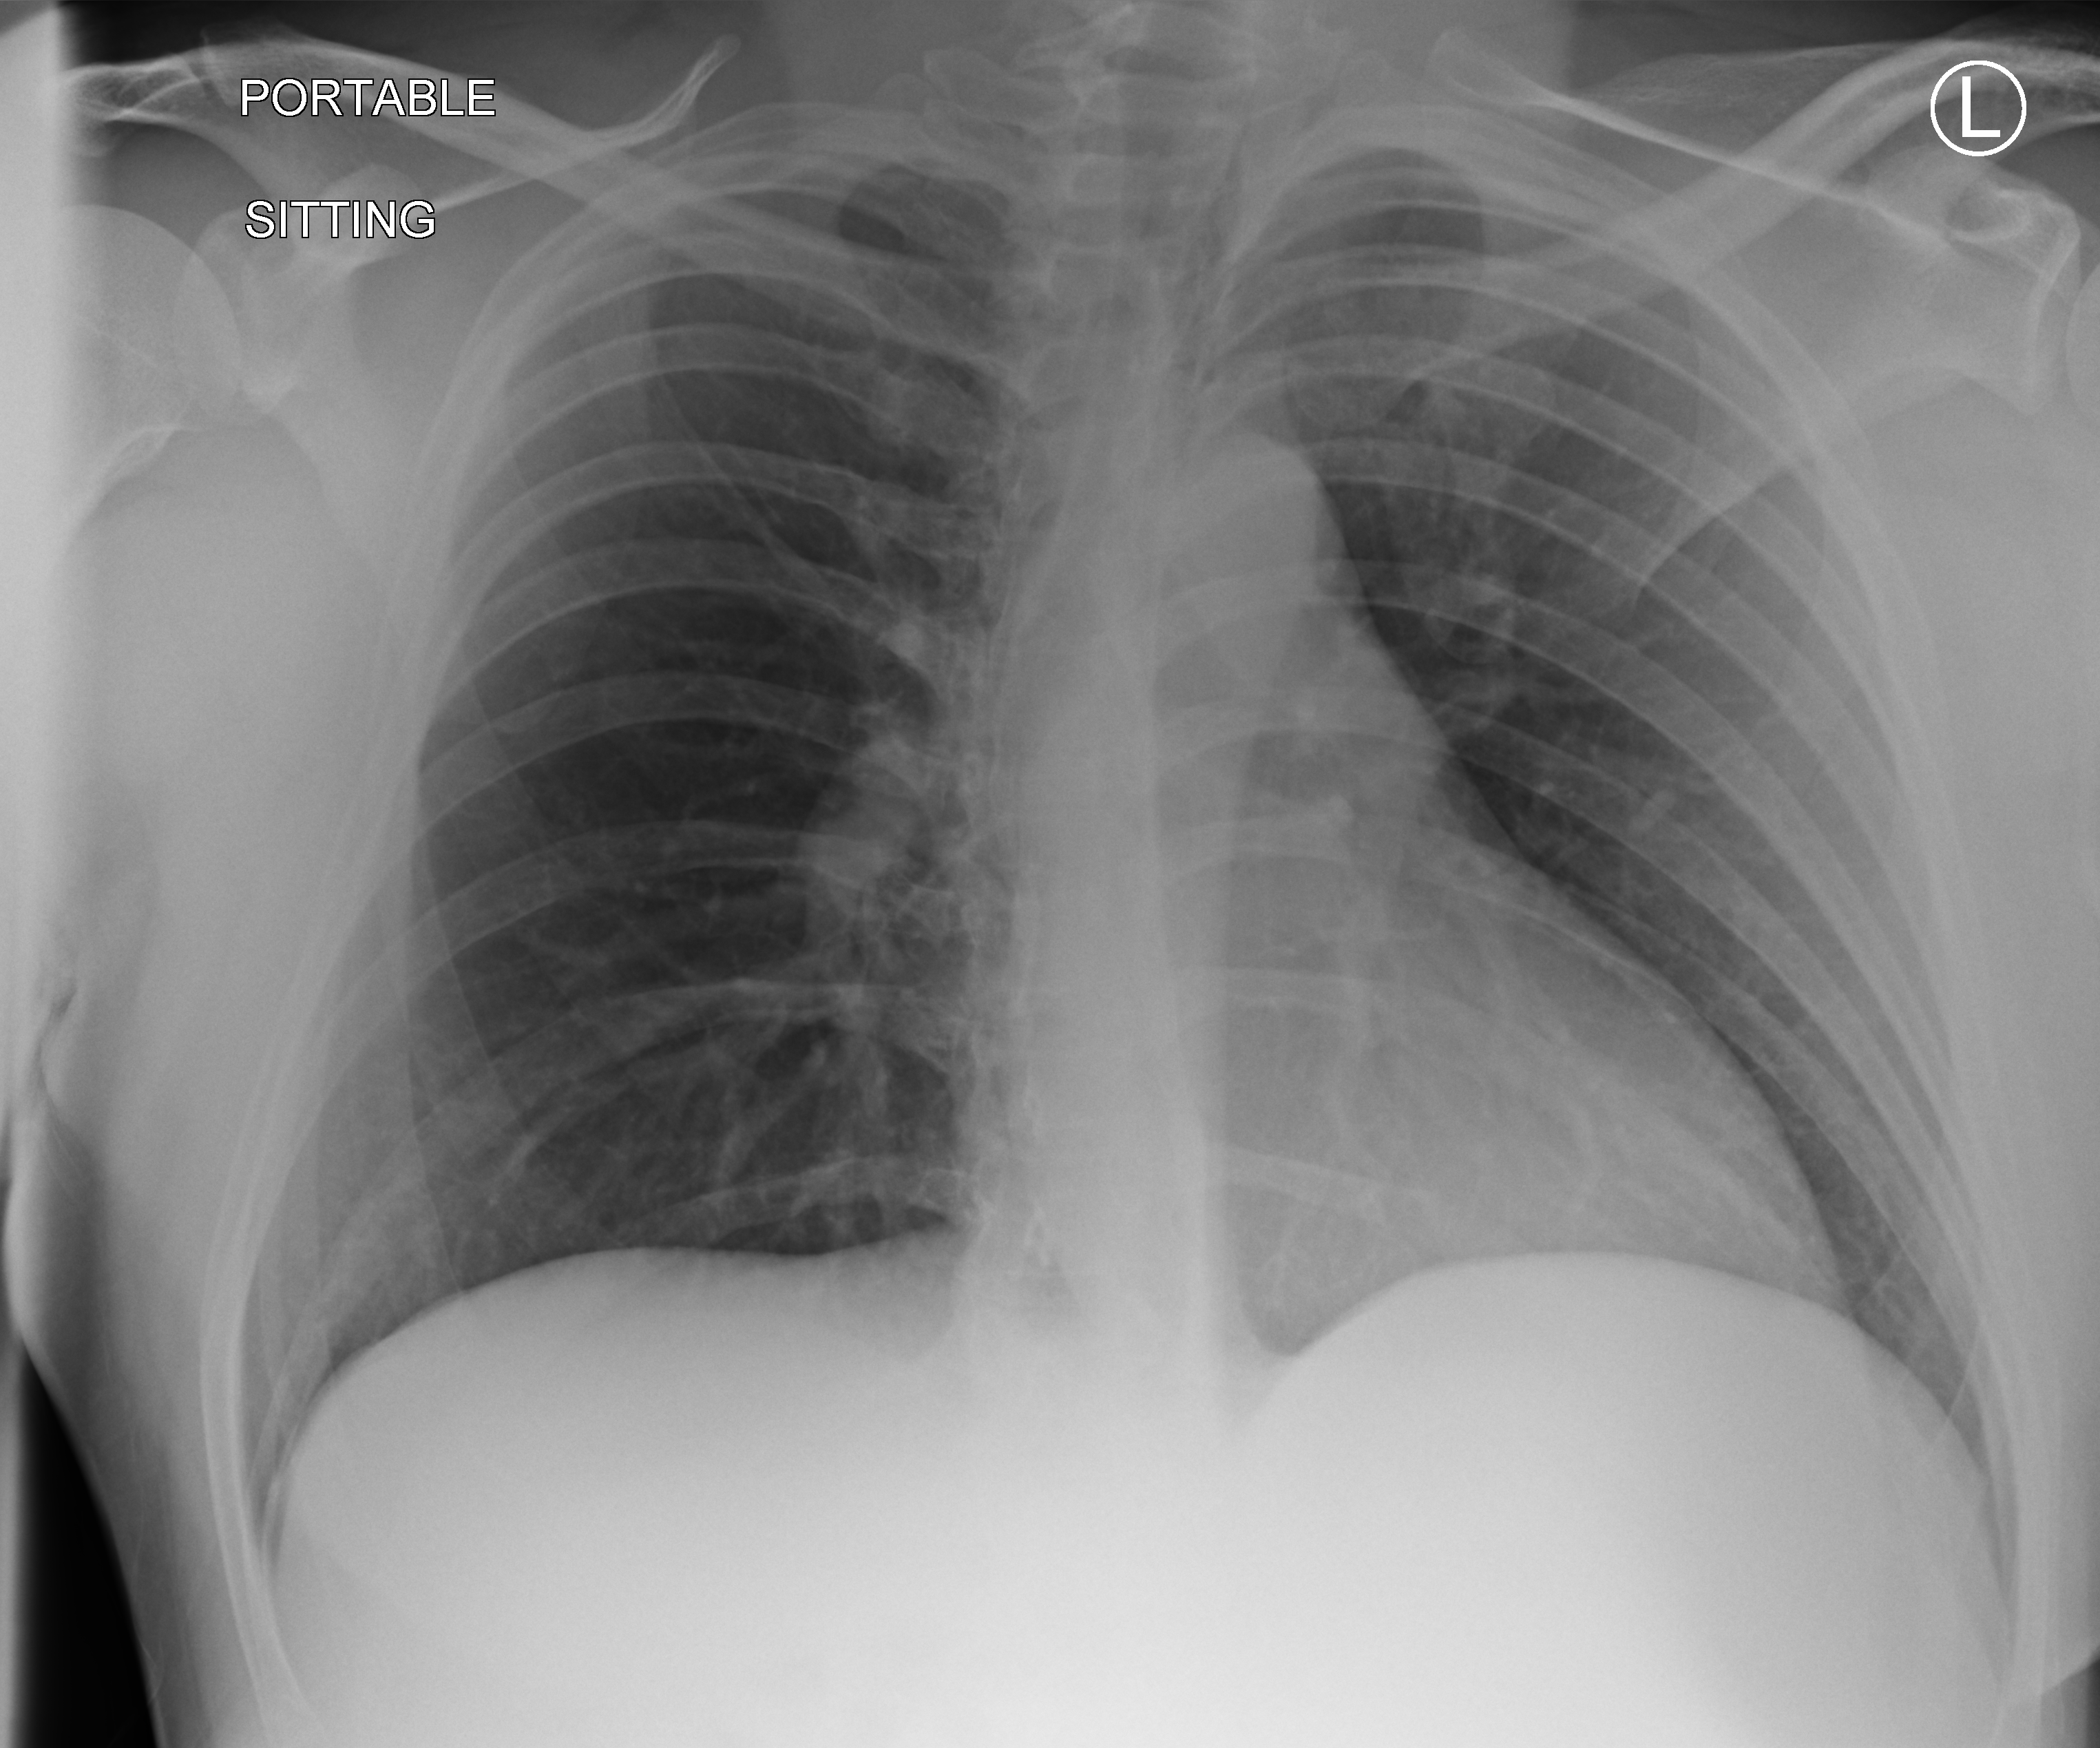
Portable chest radiograph, anteroposterior (AP) projection. Male patient hospitalised with COVID-19, age 18–59 years.
From the hospital-stay record, not from the radiograph (when in the stay this image was taken is not recorded): admitted to intensive care during this hospital stay: no.